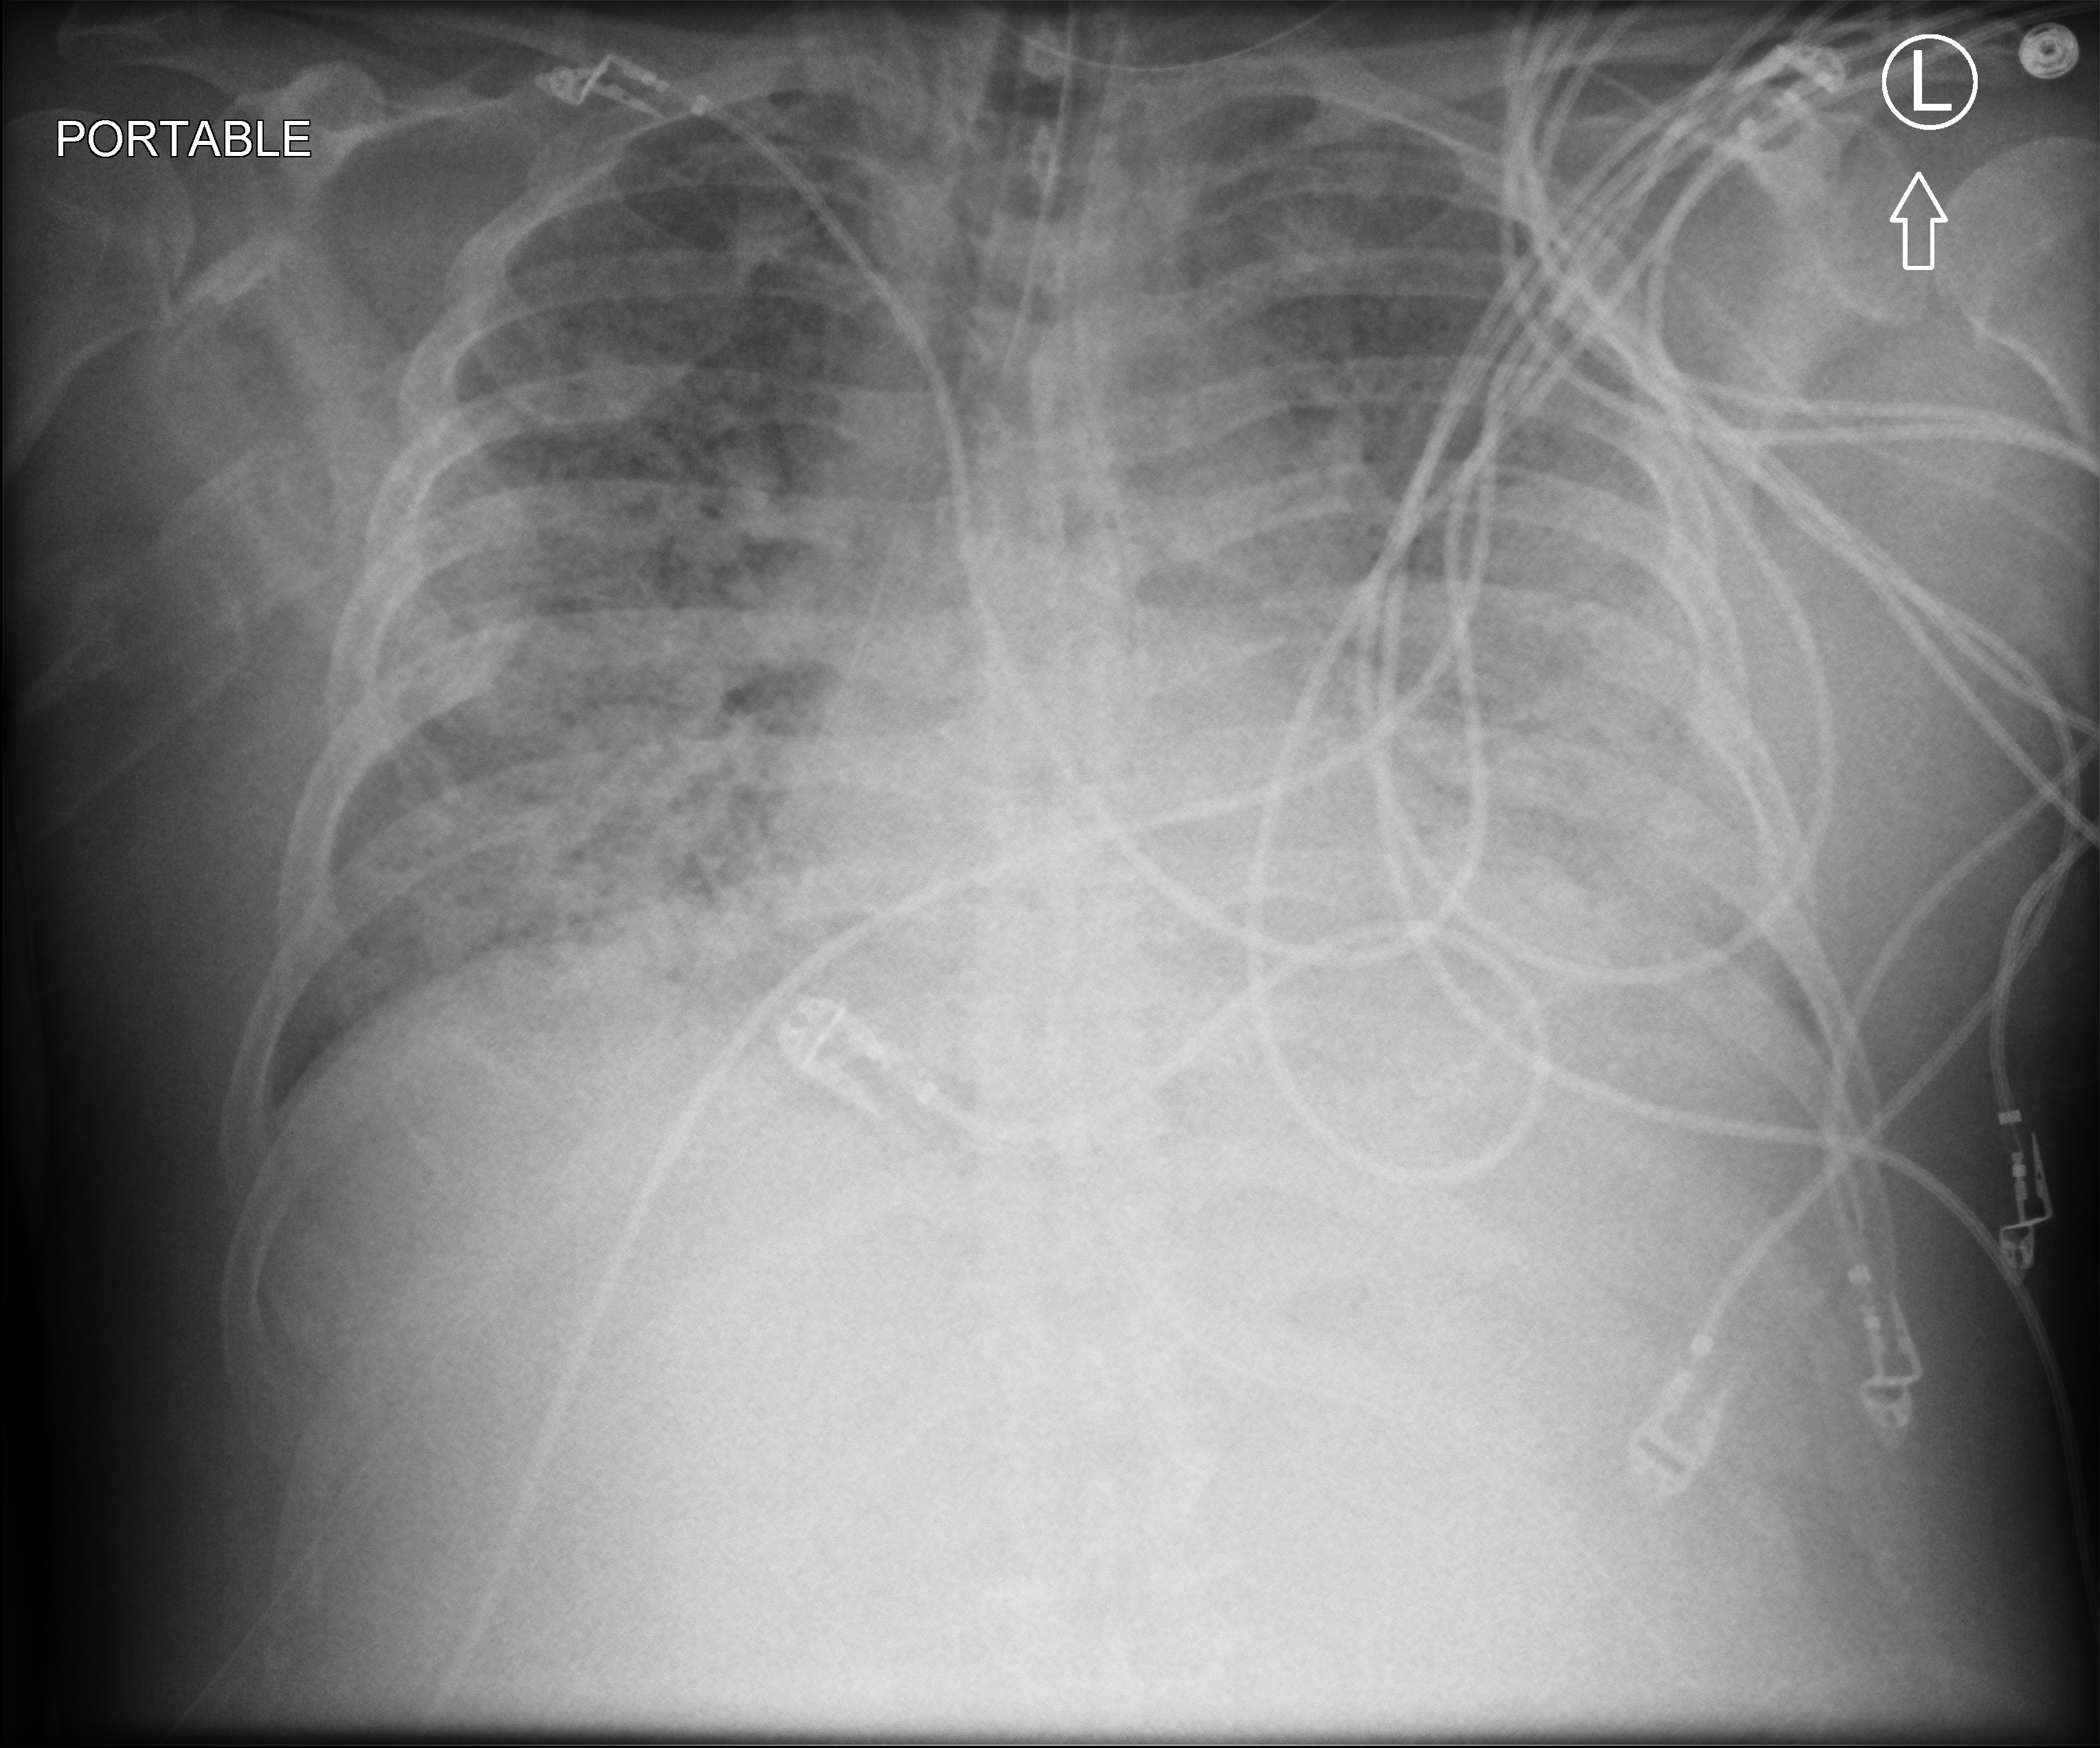
Portable chest radiograph, anteroposterior (AP) projection. Male patient hospitalised with COVID-19, age 60–74 years.
Admission-level facts for this patient (not findings on this image; timing relative to this image not recorded):
- admitted to intensive care during this hospital stay: yes
- mechanically ventilated during this hospital stay: yes
- other chronic lung disease (admission record): no